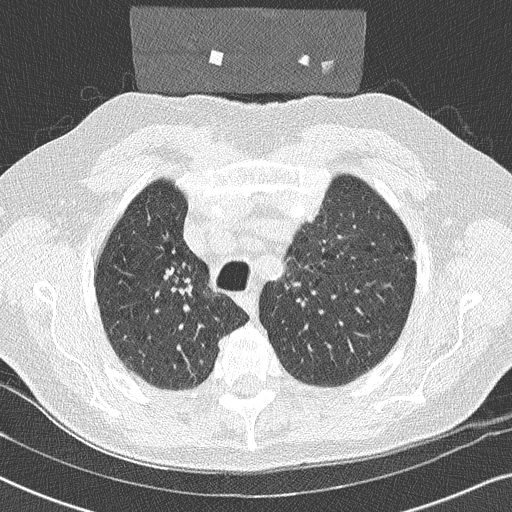
Low-dose screening chest CT, one axial slice; position 188 of 252 along the scan axis; reconstruction kernel B50f; lung window (W 1500 / L -600 HU); 2 mm slice thickness; 512 × 512 image matrix.
Annotated regions visible in this slice (outlined manually by an expert reader):
- lesion 1 (tumor, upper lobe of right lung): bounding box <174,275,180,283> (left, top, right, bottom; pixels)